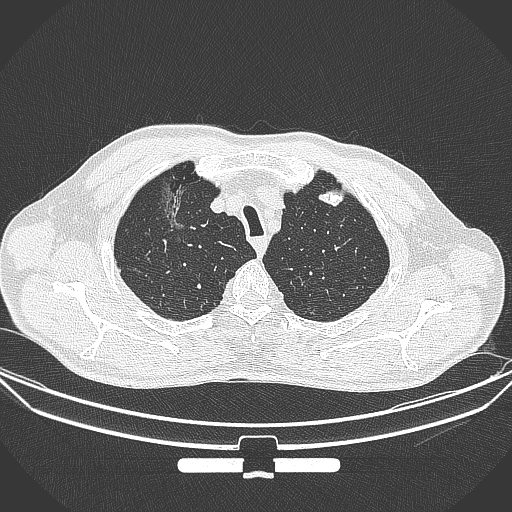
Chest CT, one axial slice; position 292 of 355 along the scan axis; lung window (W 1500 / L -600 HU); 1 mm slice thickness; 512 × 512 image matrix, field of view 399 × 399 mm. Male patient, age 67 years. Case-level facts recorded for this patient, not image findings: clinical TNM (as recorded): T1c N0 M0; histopathological grade: G2.
Annotated regions visible in this slice (bounding box drawn by a radiologist):
- lung tumour (recorded histology: adenocarcinoma): bounding box [x1, y1, x2, y2] px = [151, 177, 197, 232]